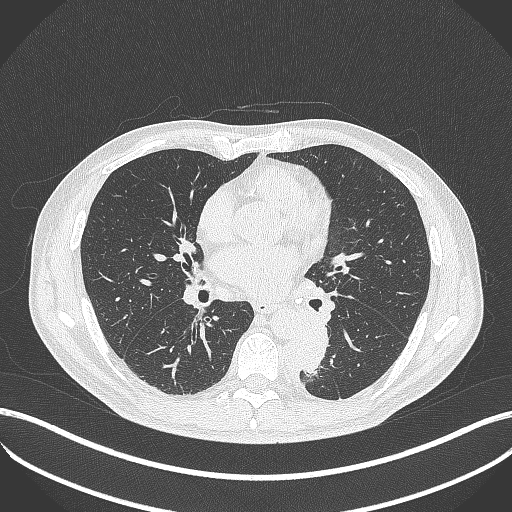
Chest CT, one axial slice. Slice 203 of 451 in the series (ordered by position). Reconstruction kernel B70f. 120 kVp. Lung window (W 1500 / L -600 HU). 1 mm slice thickness. 512 × 512 image matrix. Male patient, age 72 years. Case-level facts recorded for this patient, not image findings: clinical TNM (as recorded): T2b N0 M1.
Structures marked on this image (rectangle marked by the reading radiologist):
- lung tumour (recorded histology: adenocarcinoma): box from (x=280, y=322) to (x=330, y=383) px